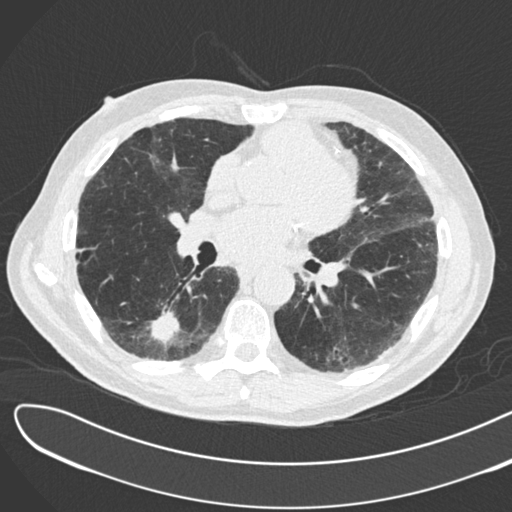
Low-dose screening chest CT, one axial slice. Slice 86 of 183 in the series (ordered by position). Reconstruction kernel B30f. 120 kVp. Lung window (W 1500 / L -600 HU). 2 mm slice thickness. 512 × 512 image matrix, field of view 370 × 370 mm.
Structures marked on this image (outlined manually by an expert reader):
- lesion 1 (tumor, lower lobe of right lung): box from (x=150, y=305) to (x=180, y=344) px